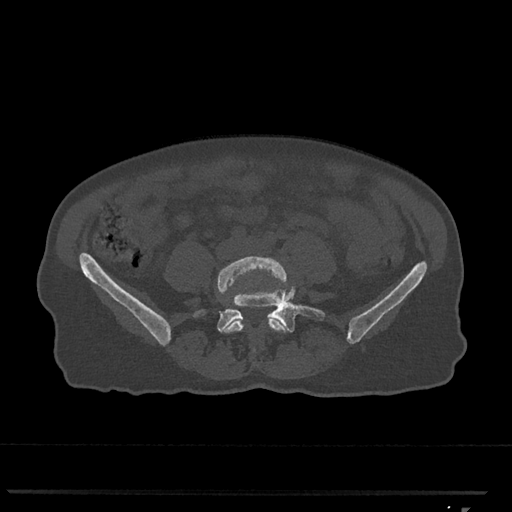
CT including the spine, one axial slice. Slice 175 of 793 in the series (ordered by position). Bone window (W 1800 / L 400 HU). 0.5 mm slice thickness. 512 × 512 image matrix, field of view 380 × 380 mm. Female patient, age 62 years. Case-level facts recorded for this patient, not image findings: primary cancer: renal.
Annotated regions visible in this slice (semi-automatic segmentation, software-assisted and operator-edited):
- L4 vertebra: bounding box [x1, y1, x2, y2] px = [217, 256, 288, 351]
- L5 vertebra: [193, 271, 326, 333]